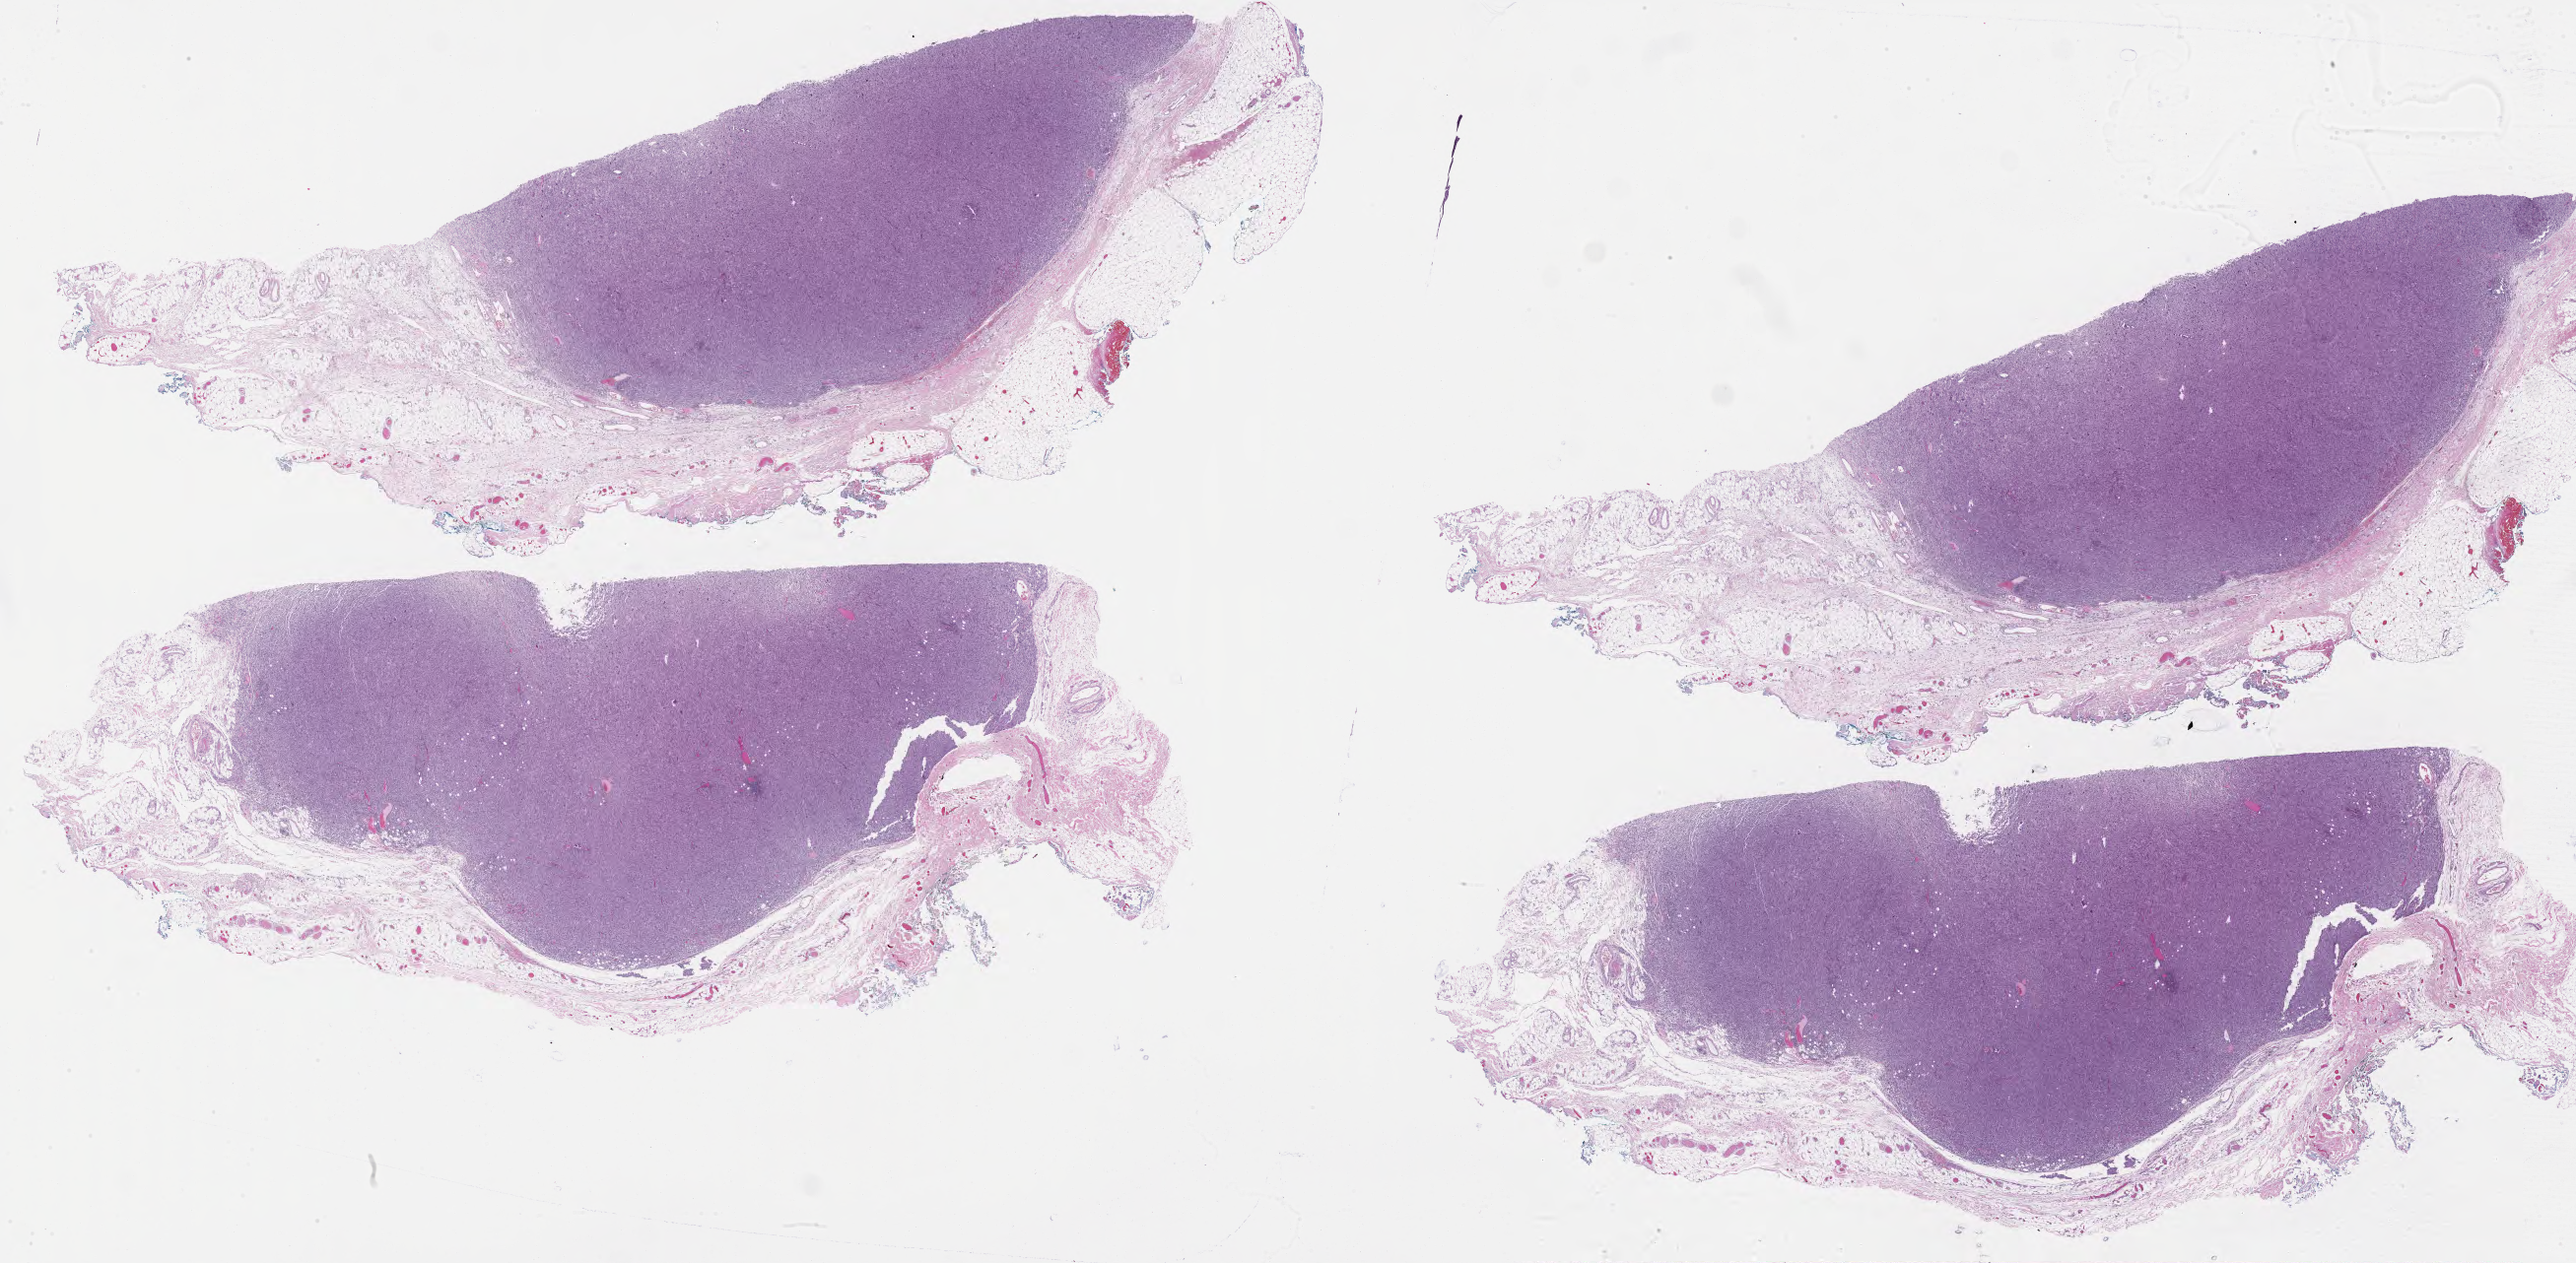
Digitized H&E-stained tissue section (whole slide), low-resolution overview of the scanned area, about 42.0 x 20.6 mm, formalin-fixed paraffin-embedded (FFPE) diagnostic section, connective, subcutaneous and other soft tissues, primary tumour sample. Patient: male, age at initial diagnosis 86 years.
Pathologic diagnosis: Undifferentiated sarcoma (connective, subcutaneous and other soft tissues of trunk, NOS).